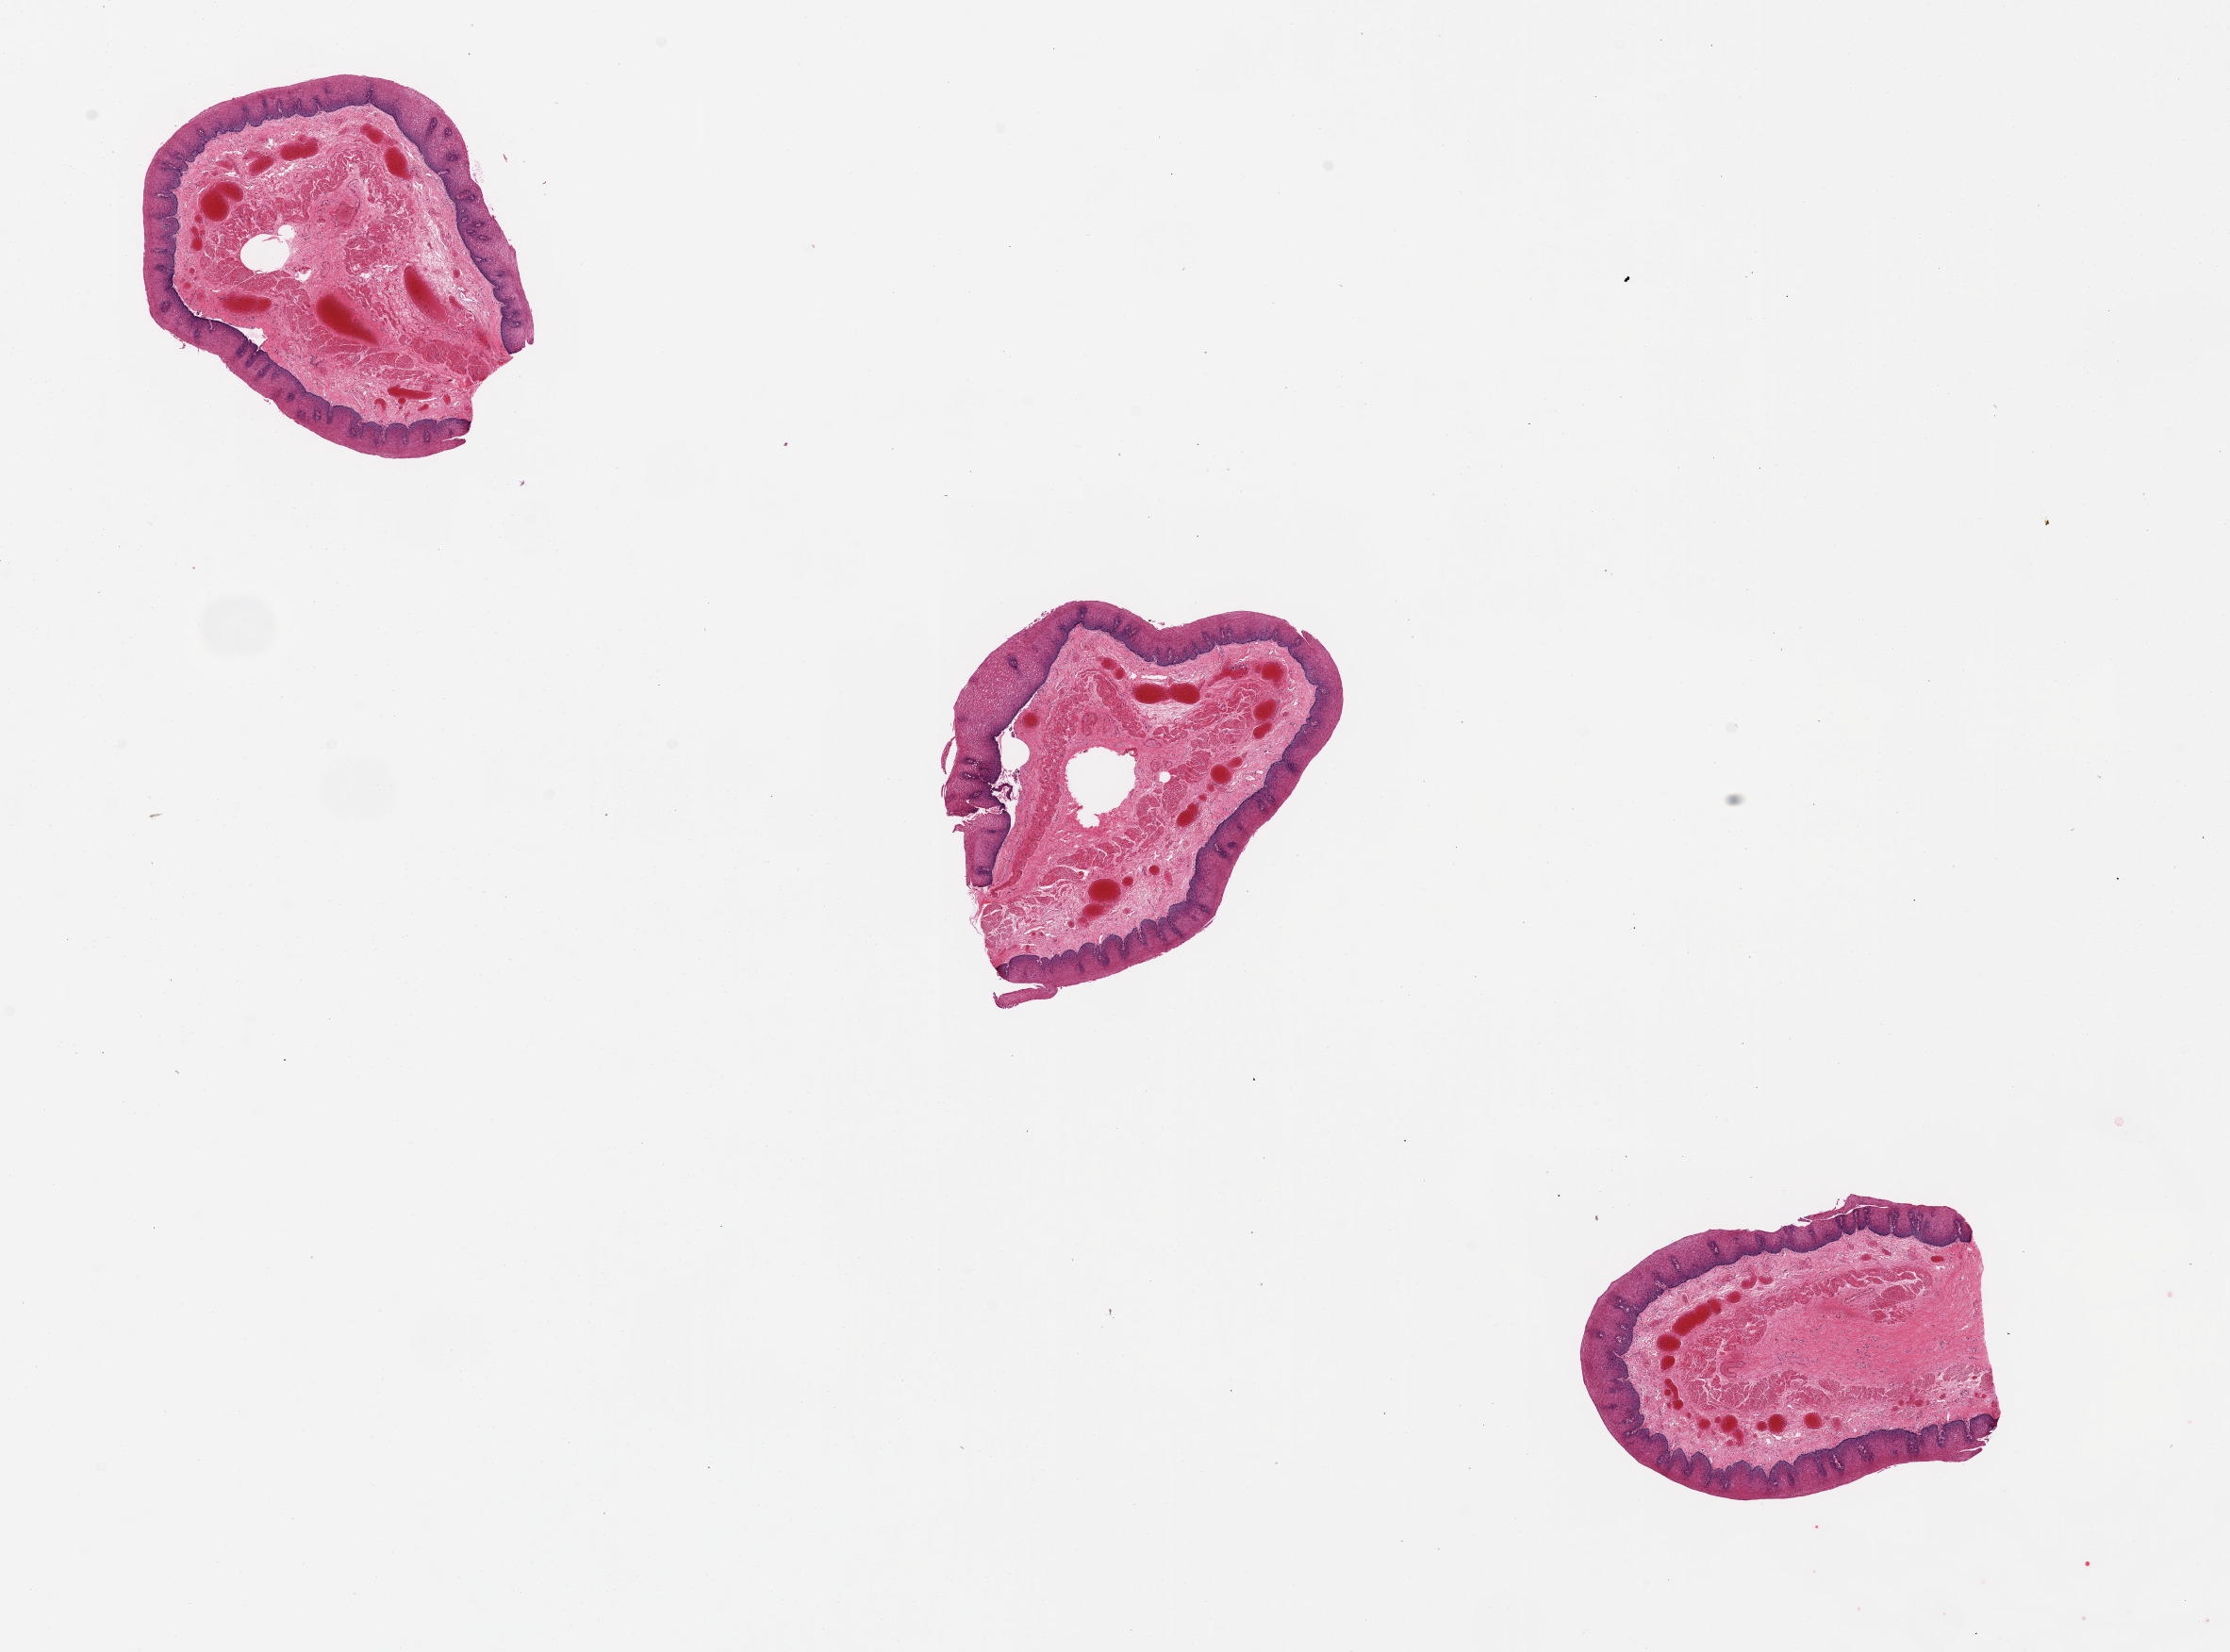
Digitized haematoxylin and eosin-stained section — shown as a low-resolution overview of the whole scanned area (about 18.7 x 13.9 mm); PAXgene-fixed paraffin-embedded (PFPE) section; target tissue: esophageal mucous membrane; tissue donor sample. Female donor.
- reviewer comment on this tissue sample: 3 pieces, adquate for analysis